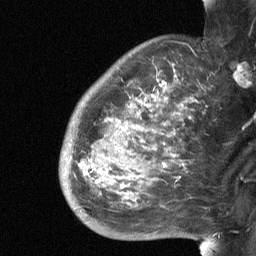
Breast MRI (dynamic contrast-enhanced), one sagittal slice; position 48 of 64 along the scan axis; dynamic contrast-enhanced study with each time point stored as its own series, time point 2 of 3 at this slice position (early post-contrast, ordered by acquisition time); 1.5 T; TE 4.8 ms, TR 27 ms; 256 × 256 image matrix, field of view 200 × 200 mm. Patient: female, 50 years. From the clinical record (not read from this slice): setting: breast cancer imaged before/during neoadjuvant chemotherapy; receptor status: HER2-positive.
Structures marked on this image (semi-automatically segmented with operator editing):
- analysis volume of interest (the breast-tissue region the enhancement analysis was run in; not a lesion): bounding box (x1, y1, x2, y2) in pixels: (59, 91, 198, 227)
- tumour enhancement mask (voxels above the 90 % enhancement threshold inside the analysis volume of interest): (79, 164, 87, 174)